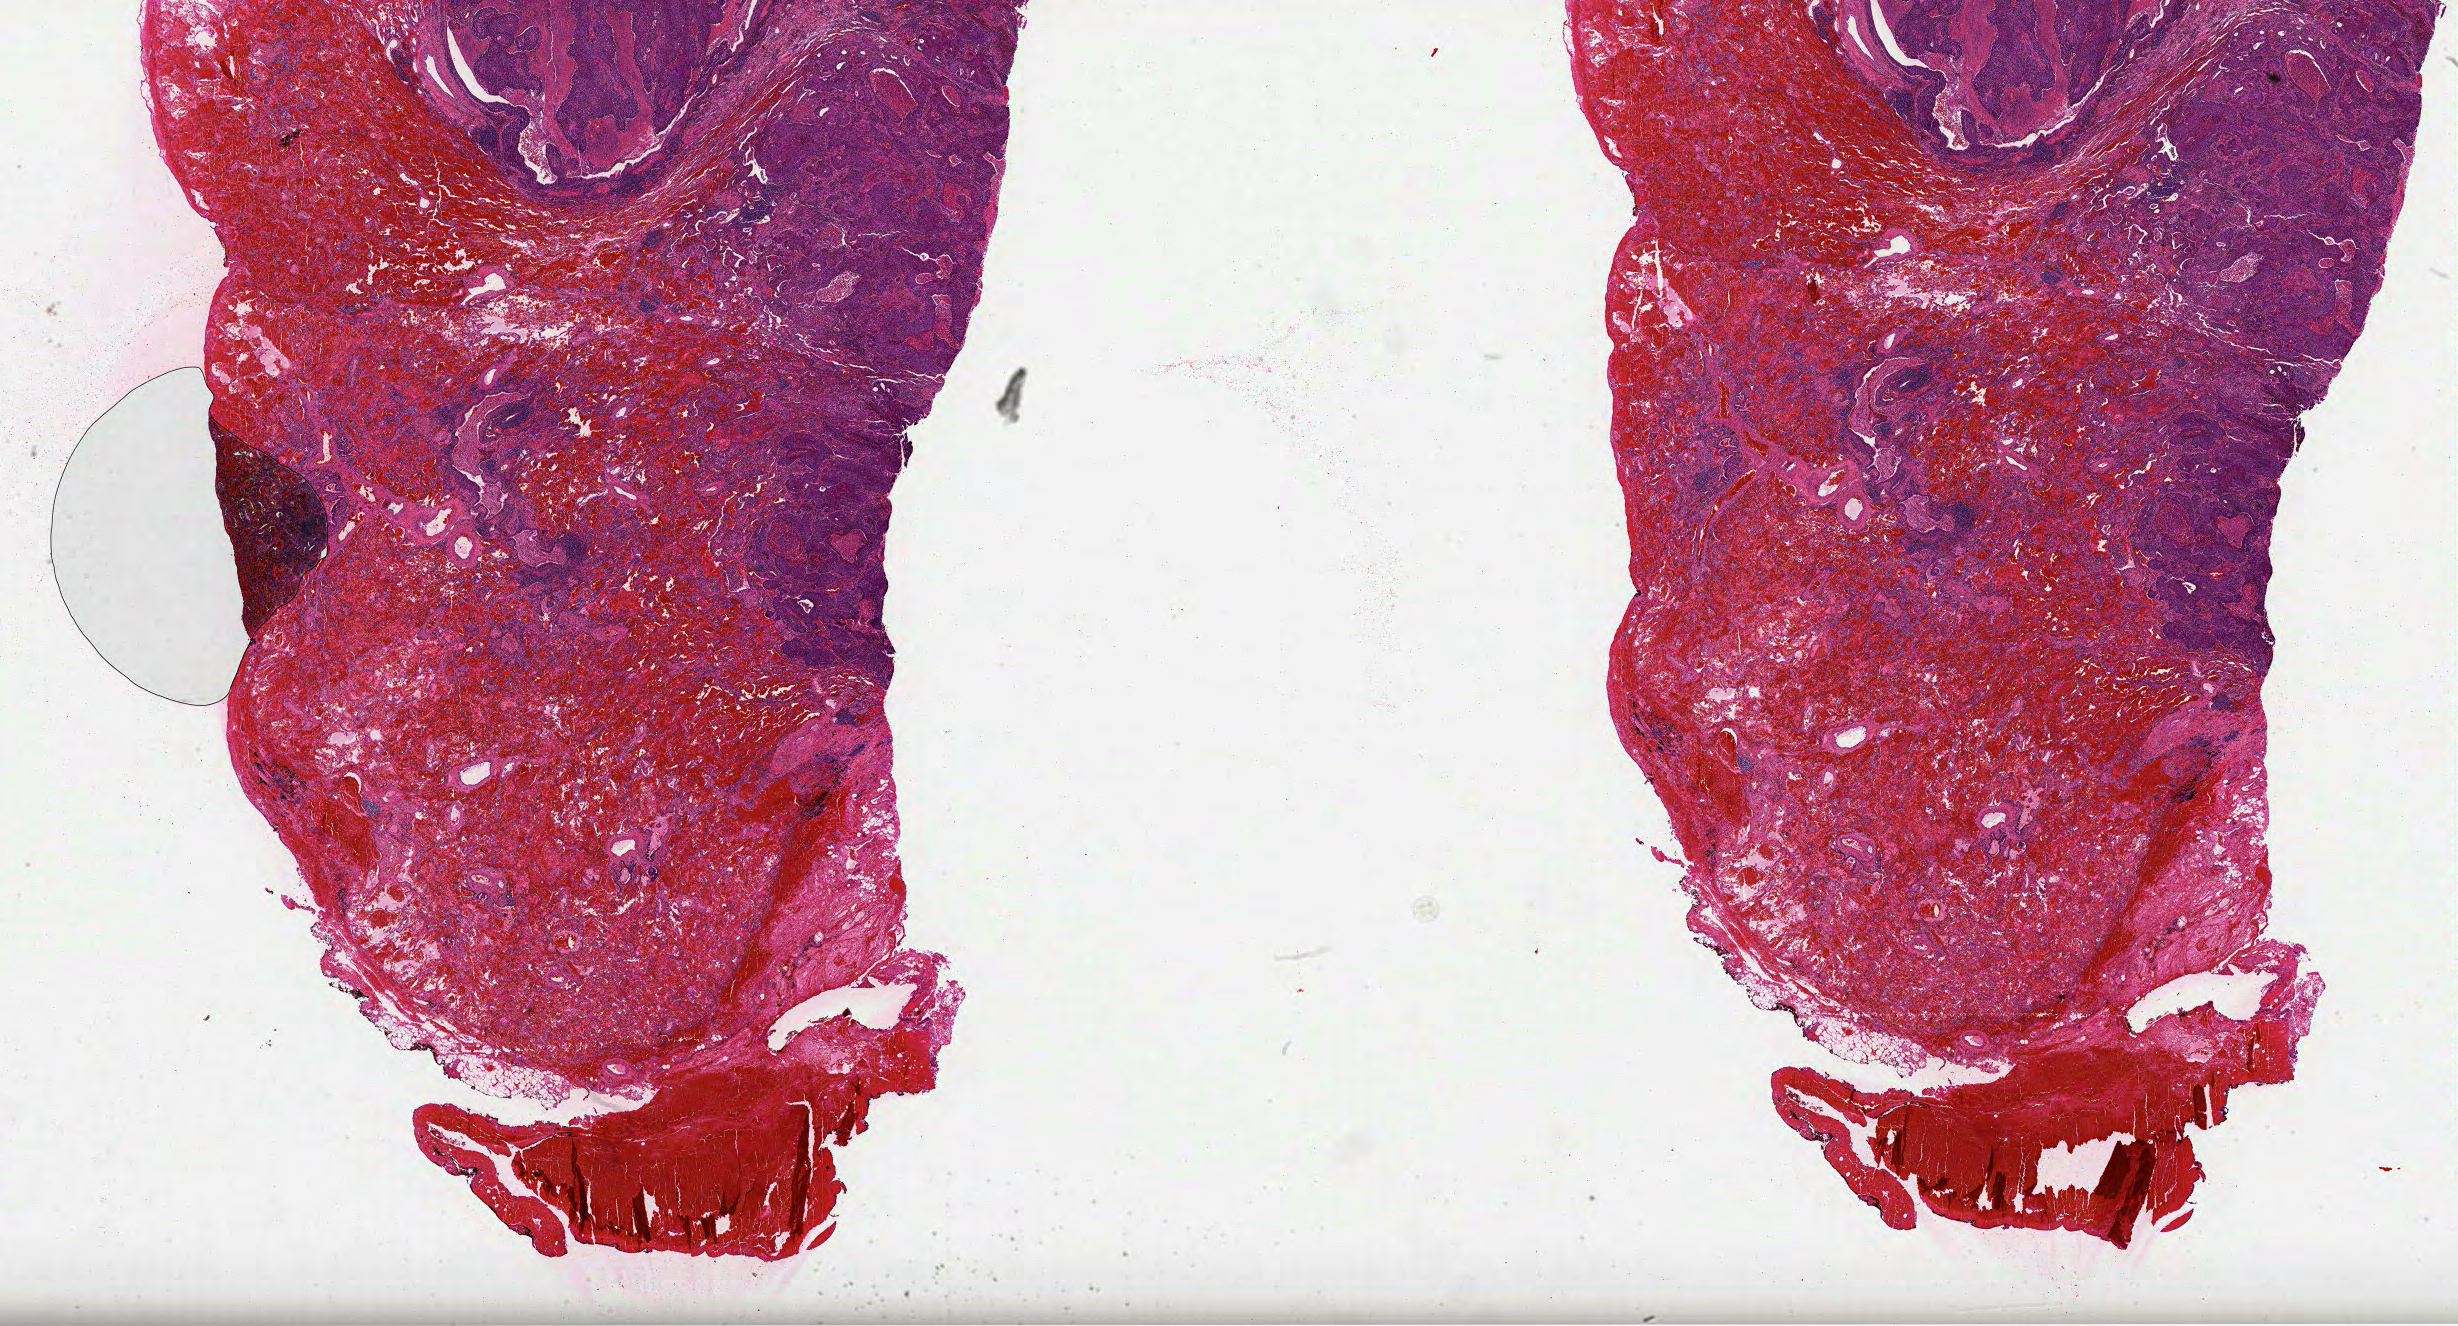
Digitized H&E-stained tissue section (whole slide) — low-resolution overview of the scanned area, about 39.6 x 21.4 mm (from a 40x scan). FFPE section. Sample: primary tumour, lung. Male patient; age at initial diagnosis 66 years.
Diagnosis: Squamous cell carcinoma, NOS (upper lobe, lung). Laterality: left. AJCC pathologic stage: IIIA (6th edition).